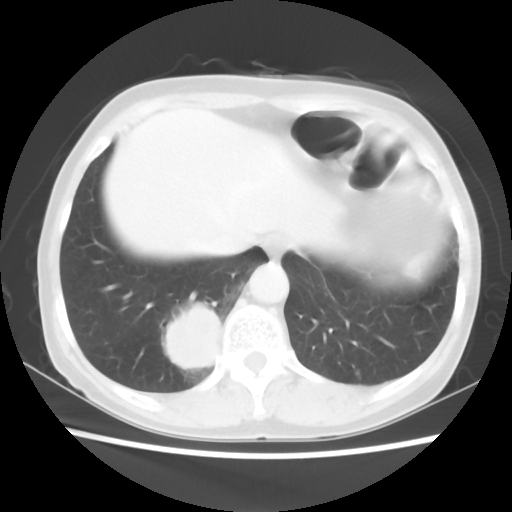
Chest CT, one axial slice. Reconstruction kernel STANDARD. Lung window (W 1500 / L -600 HU). 512 × 512 image matrix, field of view 332 × 332 mm. Patient: female, 66 years. Case-level facts recorded for this patient, not image findings: clinical TNM (as recorded): T2 N3 M0.
Structures marked on this image (rectangle marked by the reading radiologist):
- lung tumour (recorded histology: small cell carcinoma): bounding box <148,289,228,380> (left, top, right, bottom; pixels)